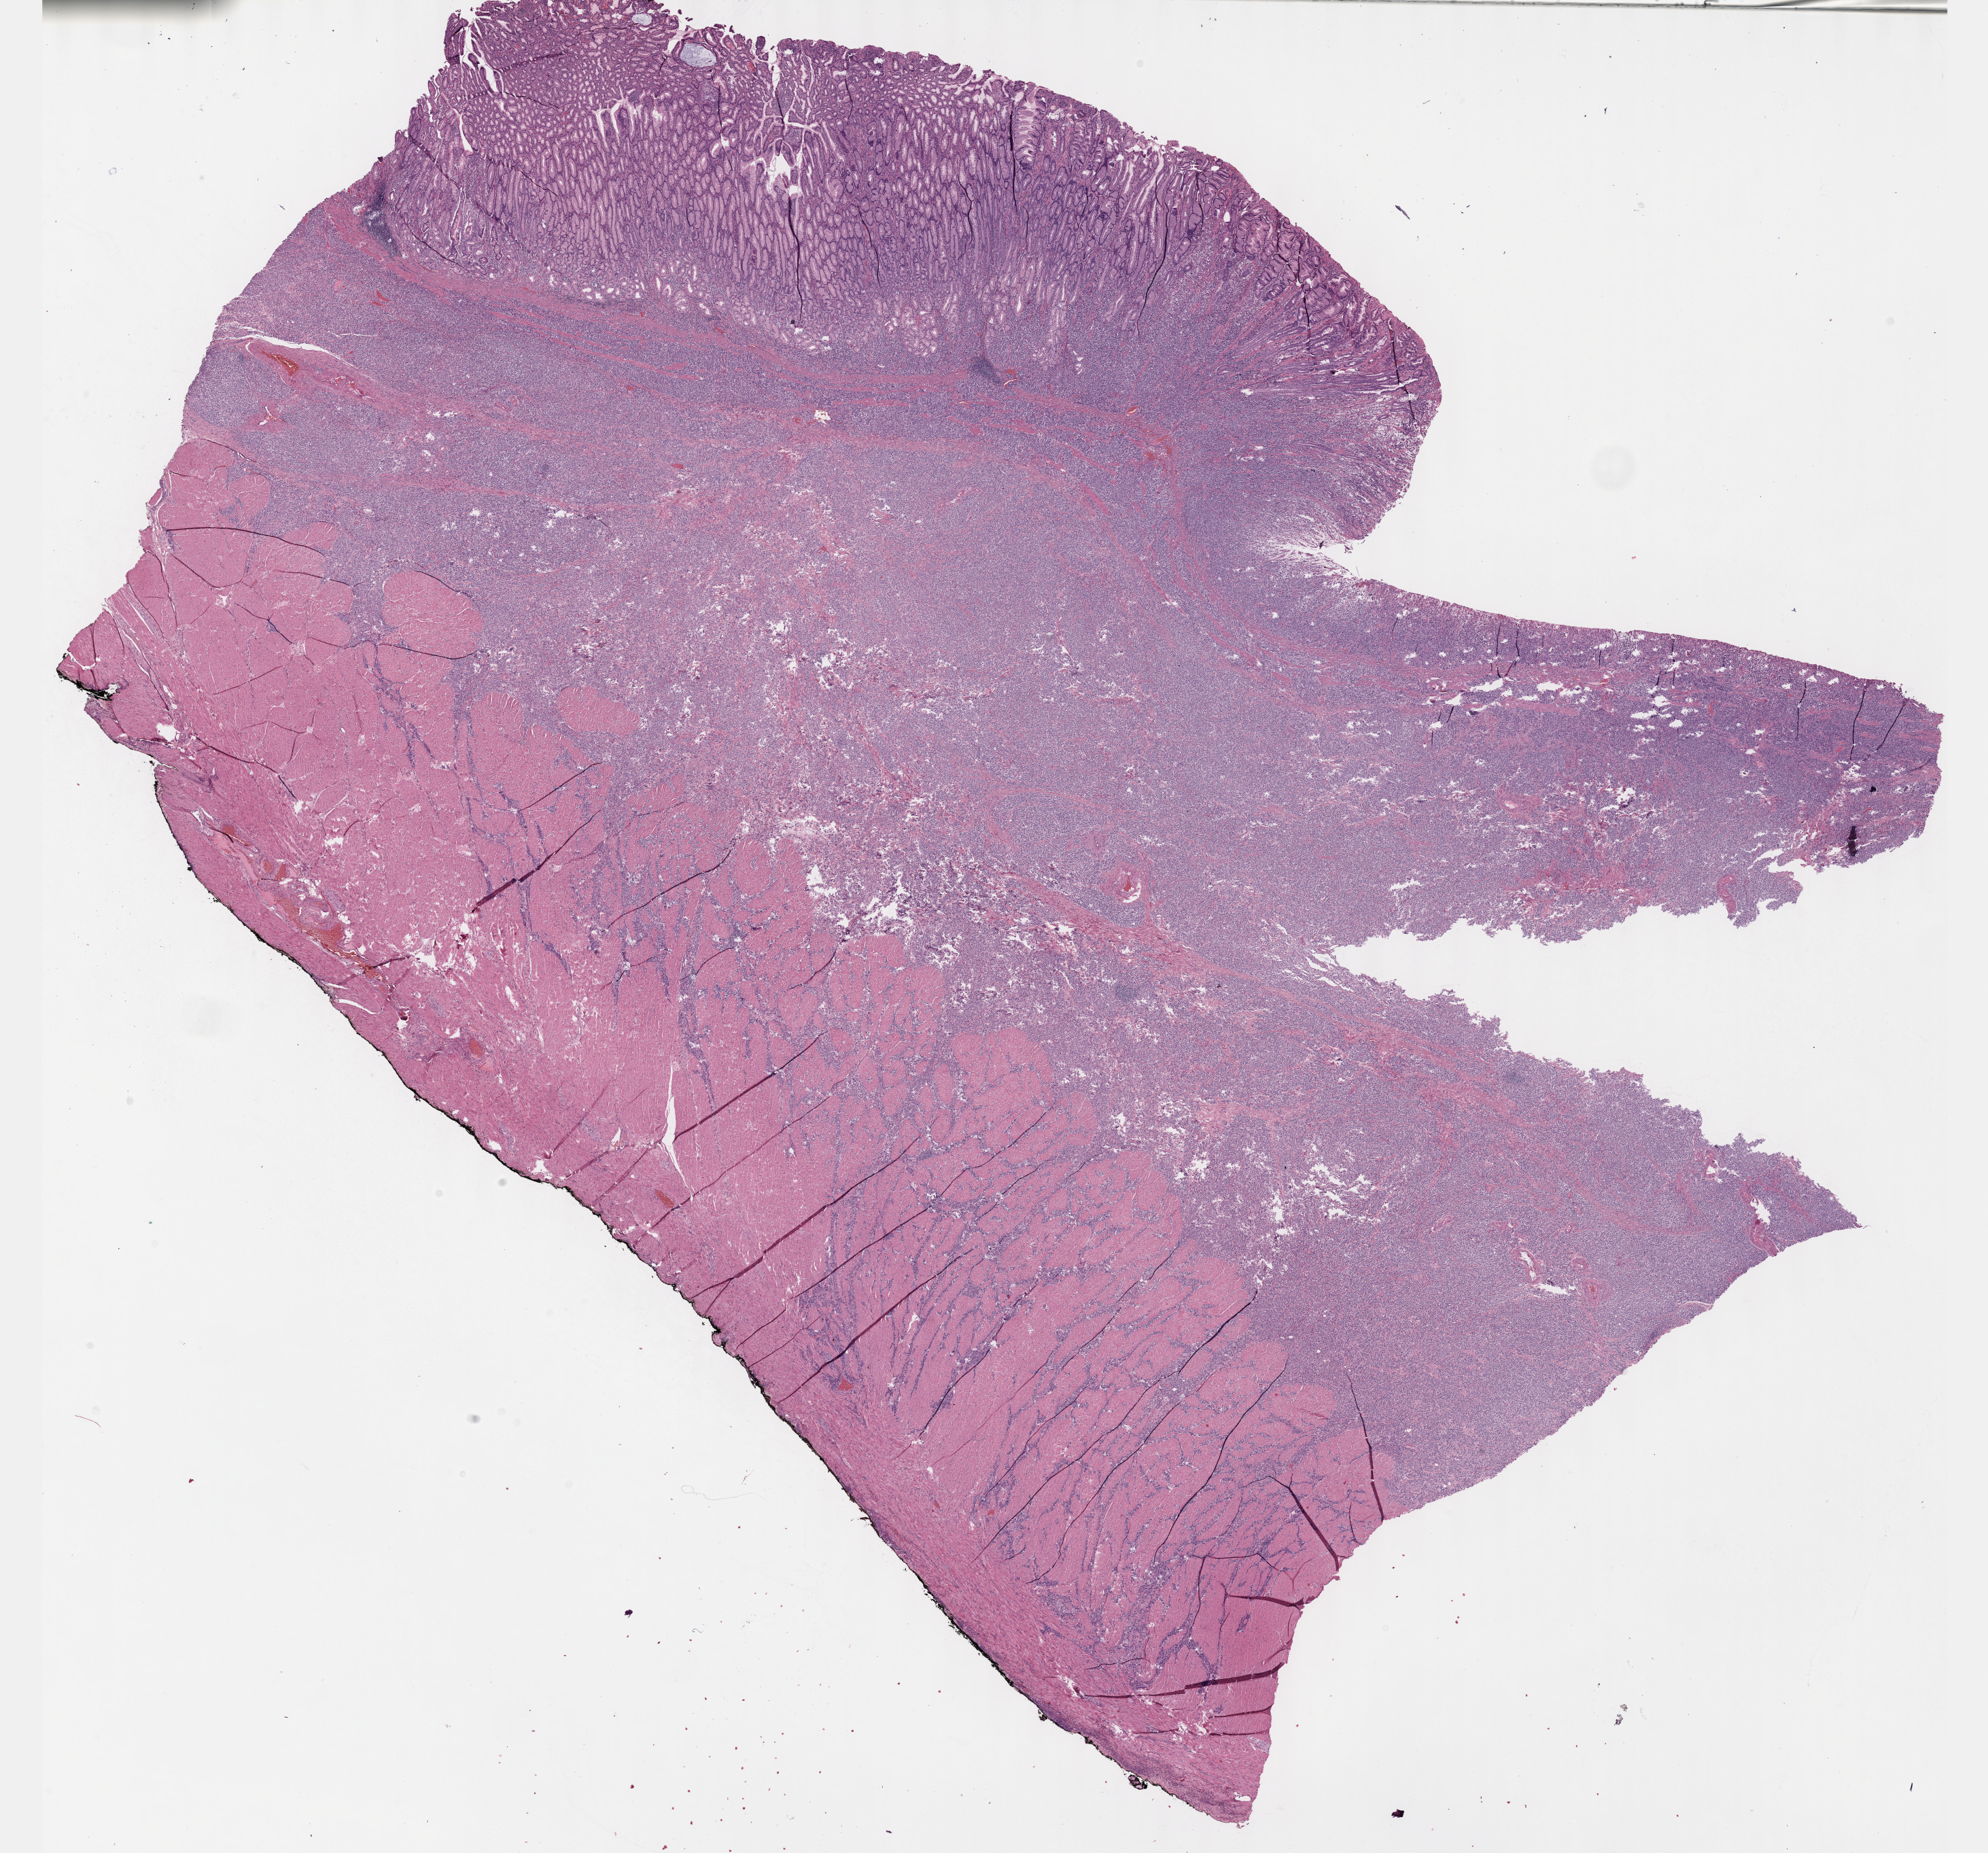
Whole-slide histology image, Hematoxylin and eosin (H&E) stained — low-resolution overview of the scanned area, about 23.6 x 22.0 mm (from a 40x scan), formalin-fixed paraffin-embedded (FFPE) diagnostic section, sample: primary tumour, stomach. Patient: male, age at initial diagnosis 70 years.
Histologic diagnosis: Signet ring cell carcinoma.